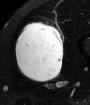
MRI of an extremity soft-tissue mass, one axial slice; position 30 of 65 along the scan axis; T2-weighted fat-saturated; MR volume resampled by the dataset authors to the PET/CT grid (not the native acquisition matrix); 90 × 105 image matrix. Male patient. Case-level facts recorded for this patient, not image findings: histological type: mixoid liposarcoma; grade: low; site of the primary tumour: left thigh.
Outlined on this slice (expert contour drawn on MRI and transferred to this co-registered scan by the dataset authors):
- gross tumour volume (mass): bounding box <14,21,63,81> (left, top, right, bottom; pixels)